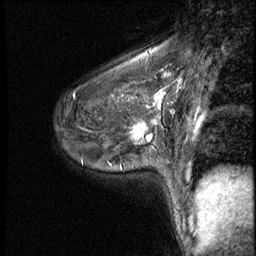
Breast MRI (dynamic contrast-enhanced), one sagittal slice. Slice 37 of 50 in the series (ordered by position). 3 images stored at this slice position (order not interpretable as contrast timing). 1.5 T. TE 4.2 ms, TR 8.7 ms. 2.5 mm slice thickness. 256 × 256 image matrix, field of view 180 × 180 mm. Patient: female, 43 years. Case-level facts recorded for this patient, not image findings: setting: breast cancer imaged before/during neoadjuvant chemotherapy; receptor status: HR-positive, HER2-negative.
Structures marked on this image (semi-automatic segmentation, software-assisted and operator-edited):
- analysis volume of interest (the breast-tissue region the enhancement analysis was run in; not a lesion): bounding box [x1, y1, x2, y2] px = [122, 109, 159, 155]
- tumour enhancement mask (voxels above the 140 % enhancement threshold inside the analysis volume of interest): [132, 120, 158, 141]